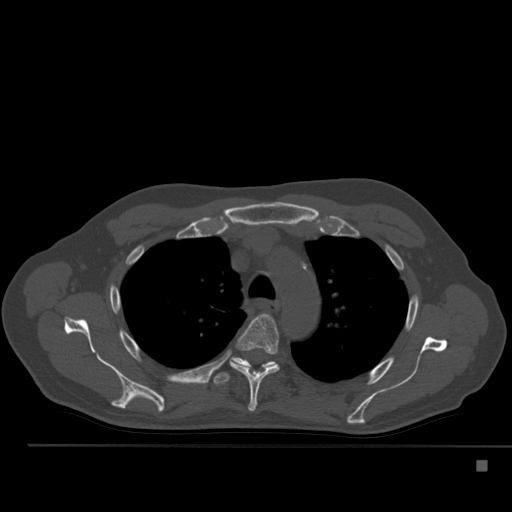
CT including the spine, one axial slice; slice 378 of 517 in the series (ordered by position); reconstruction kernel Br40s; 120 kVp; bone window (W 1800 / L 400 HU); 1.5 mm slice thickness; 512 × 512 image matrix. Male patient, age 70 years. From the clinical record (not read from this slice): primary cancer: renal.
Structures marked on this image (semi-automatic segmentation, software-assisted and operator-edited):
- T4 vertebra: box from (x=230, y=314) to (x=280, y=412) px
- T5 vertebra: (x=213, y=357)–(x=277, y=385)